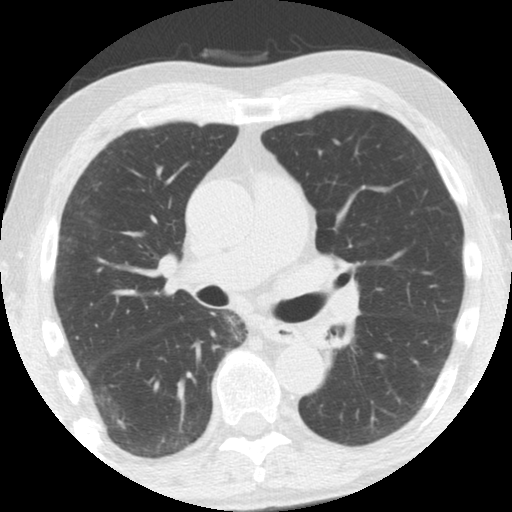
Low-dose screening chest CT, axial slice; third annual screen; lung window (W 1500 / L -600 HU); 2.5 mm slice thickness; standard (soft-tissue) reconstruction kernel (STANDARD); slice 54 of 108 in the series; 512 × 512 image matrix, field of view 308 × 308 mm. Male participant, aged 61 years at enrolment. Former smoker at enrolment.
Expert reader's lesion annotation, bounding box (x1, y1, x2, y2) in pixels: (293, 316, 344, 362). No non-calcified nodule or mass ≥4 mm was recorded by the screening reader at this exam. Participant outcome: lung cancer diagnosed 363 days after this screen — squamous cell carcinoma, NOS, left upper lobe, left lower lobe, well differentiated (G1), stage IIB (AJCC 6th edition), 100 mm at pathology.